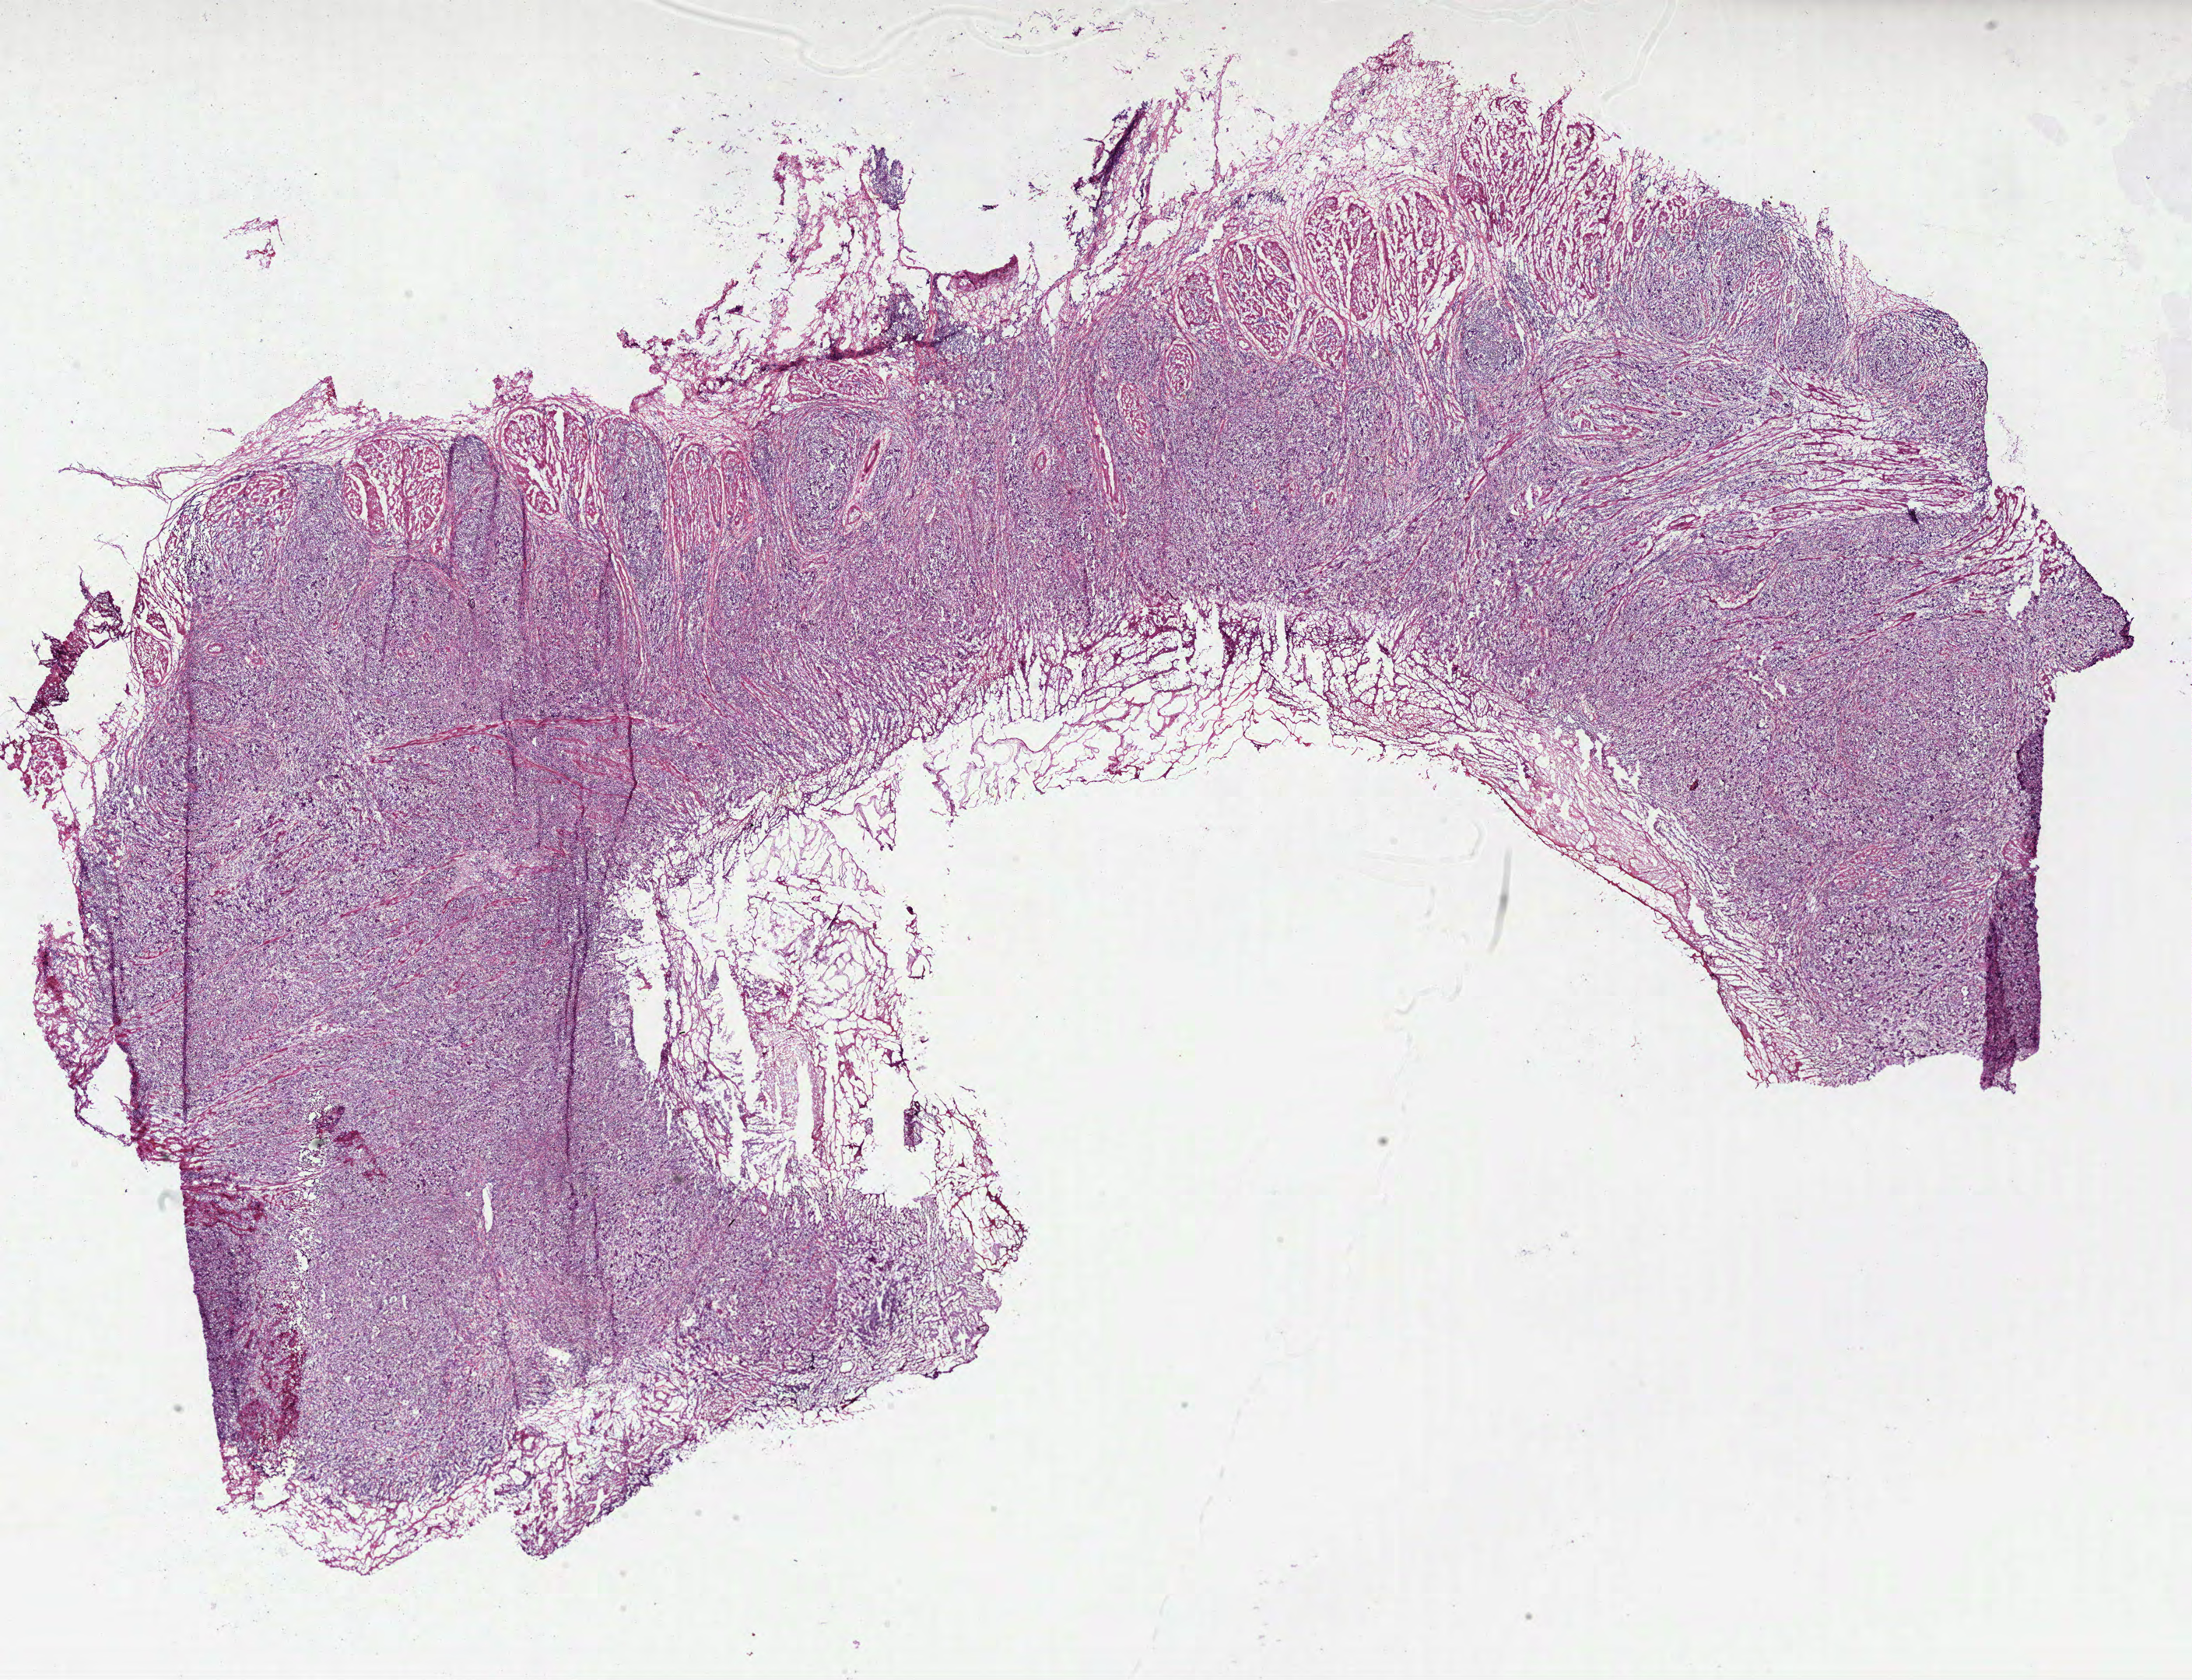
H&E whole-slide image — whole scanned area (about 22.7 x 17.4 mm, slide scanned at 40x) shown as a low-resolution overview. Frozen section. Primary tumour sample from the stomach. Patient: male, age at initial diagnosis 60 years. Histologic grade: G3 (poorly differentiated). Composition of this section per pathologist review: tumour cells 90%, tumour nuclei 60%, normal cells 0%, stromal cells 10%, necrosis 0%.
Pathologic diagnosis: Adenocarcinoma, NOS. AJCC pathologic stage: IIIB. Lymph nodes positive (case pathology): 0 of 4 examined.